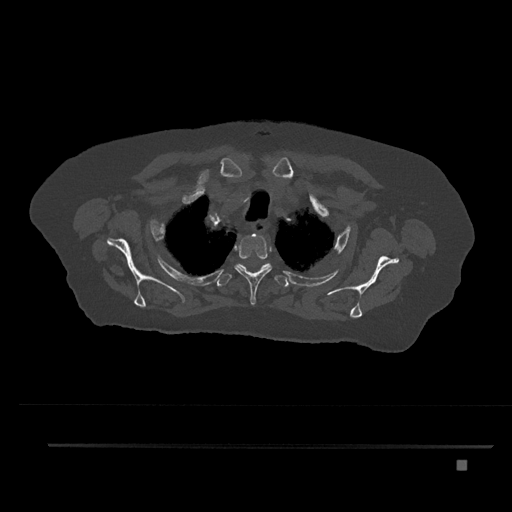
CT including the spine, one axial slice; position 661 of 797 along the scan axis; bone window (W 1800 / L 400 HU); 0.5 mm slice thickness; 512 × 512 image matrix, field of view 437 × 437 mm. Patient: female, 76 years. From the clinical record (not read from this slice): primary cancer: lung; vertebrae with lytic lesions (as recorded): T11, L3.
Annotated regions visible in this slice (semi-automatic segmentation, software-assisted and operator-edited):
- T1 vertebra: bounding box (x1, y1, x2, y2) in pixels: (252, 233, 256, 236)
- T2 vertebra: (234, 233, 272, 305)
- T3 vertebra: (217, 263, 289, 287)